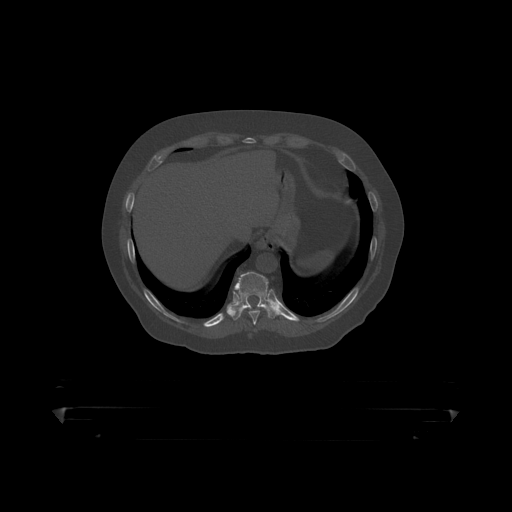
CT including the spine, one axial slice; bone window (W 1800 / L 400 HU); 1.25 mm slice thickness; 512 × 512 image matrix, field of view 650 × 650 mm. Patient: male, 60 years. Case-level facts recorded for this patient, not image findings: primary cancer: prostate.
Outlined on this slice (semi-automatically segmented with operator editing):
- T10 vertebra: box from (x=235, y=272) to (x=279, y=318) px
- T9 vertebra: (x=246, y=305)–(x=264, y=319)